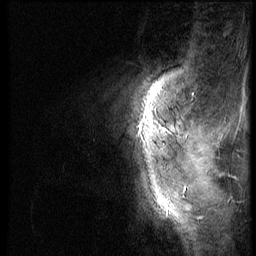
Breast MRI (dynamic contrast-enhanced), one sagittal slice. Slice 10 of 56 in the series (ordered by position). Dynamic contrast-enhanced series, image 2 of 3 at this slice position (ordered by acquisition). 1.5 T. TE 4.2 ms, TR 9 ms. 256 × 256 image matrix, field of view 180 × 180 mm. Patient: female, 46 years. Case-level facts recorded for this patient, not image findings: setting: breast cancer imaged before/during neoadjuvant chemotherapy; receptor status: HER2-positive.
Outlined on this slice (semi-automatically segmented with operator editing):
- analysis volume of interest (the breast-tissue region the enhancement analysis was run in; not a lesion): bounding box [x1, y1, x2, y2] px = [100, 98, 174, 182]
- tumour enhancement mask (voxels above the 140 % enhancement threshold inside the analysis volume of interest): [164, 128, 169, 131]